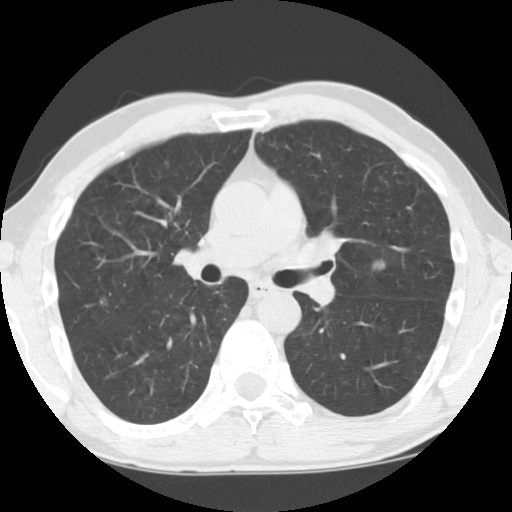
Low-dose screening chest CT, axial slice, baseline annual screen, lung window (W 1500 / L -600 HU), 2.5 mm slice thickness, standard (soft-tissue) reconstruction kernel (STANDARD), 120 kVp, 512 × 512 image matrix, field of view 320 × 320 mm. Male, age 55 years at enrolment. Current smoker at enrolment.
Expert-annotated lung lesion, bounding box <352,250,399,292> (left, top, right, bottom; pixels). The screening reader recorded 5 non-calcified nodules or masses ≥4 mm on this exam (left upper lobe, left upper lobe, right upper lobe, right upper lobe, left upper lobe); which of them this box marks is not recorded. Official screen result: positive, change unspecified: nodule(s) >= 4 mm or enlarging nodule(s), mass(es), or other non-specific abnormalities suspicious for lung cancer.